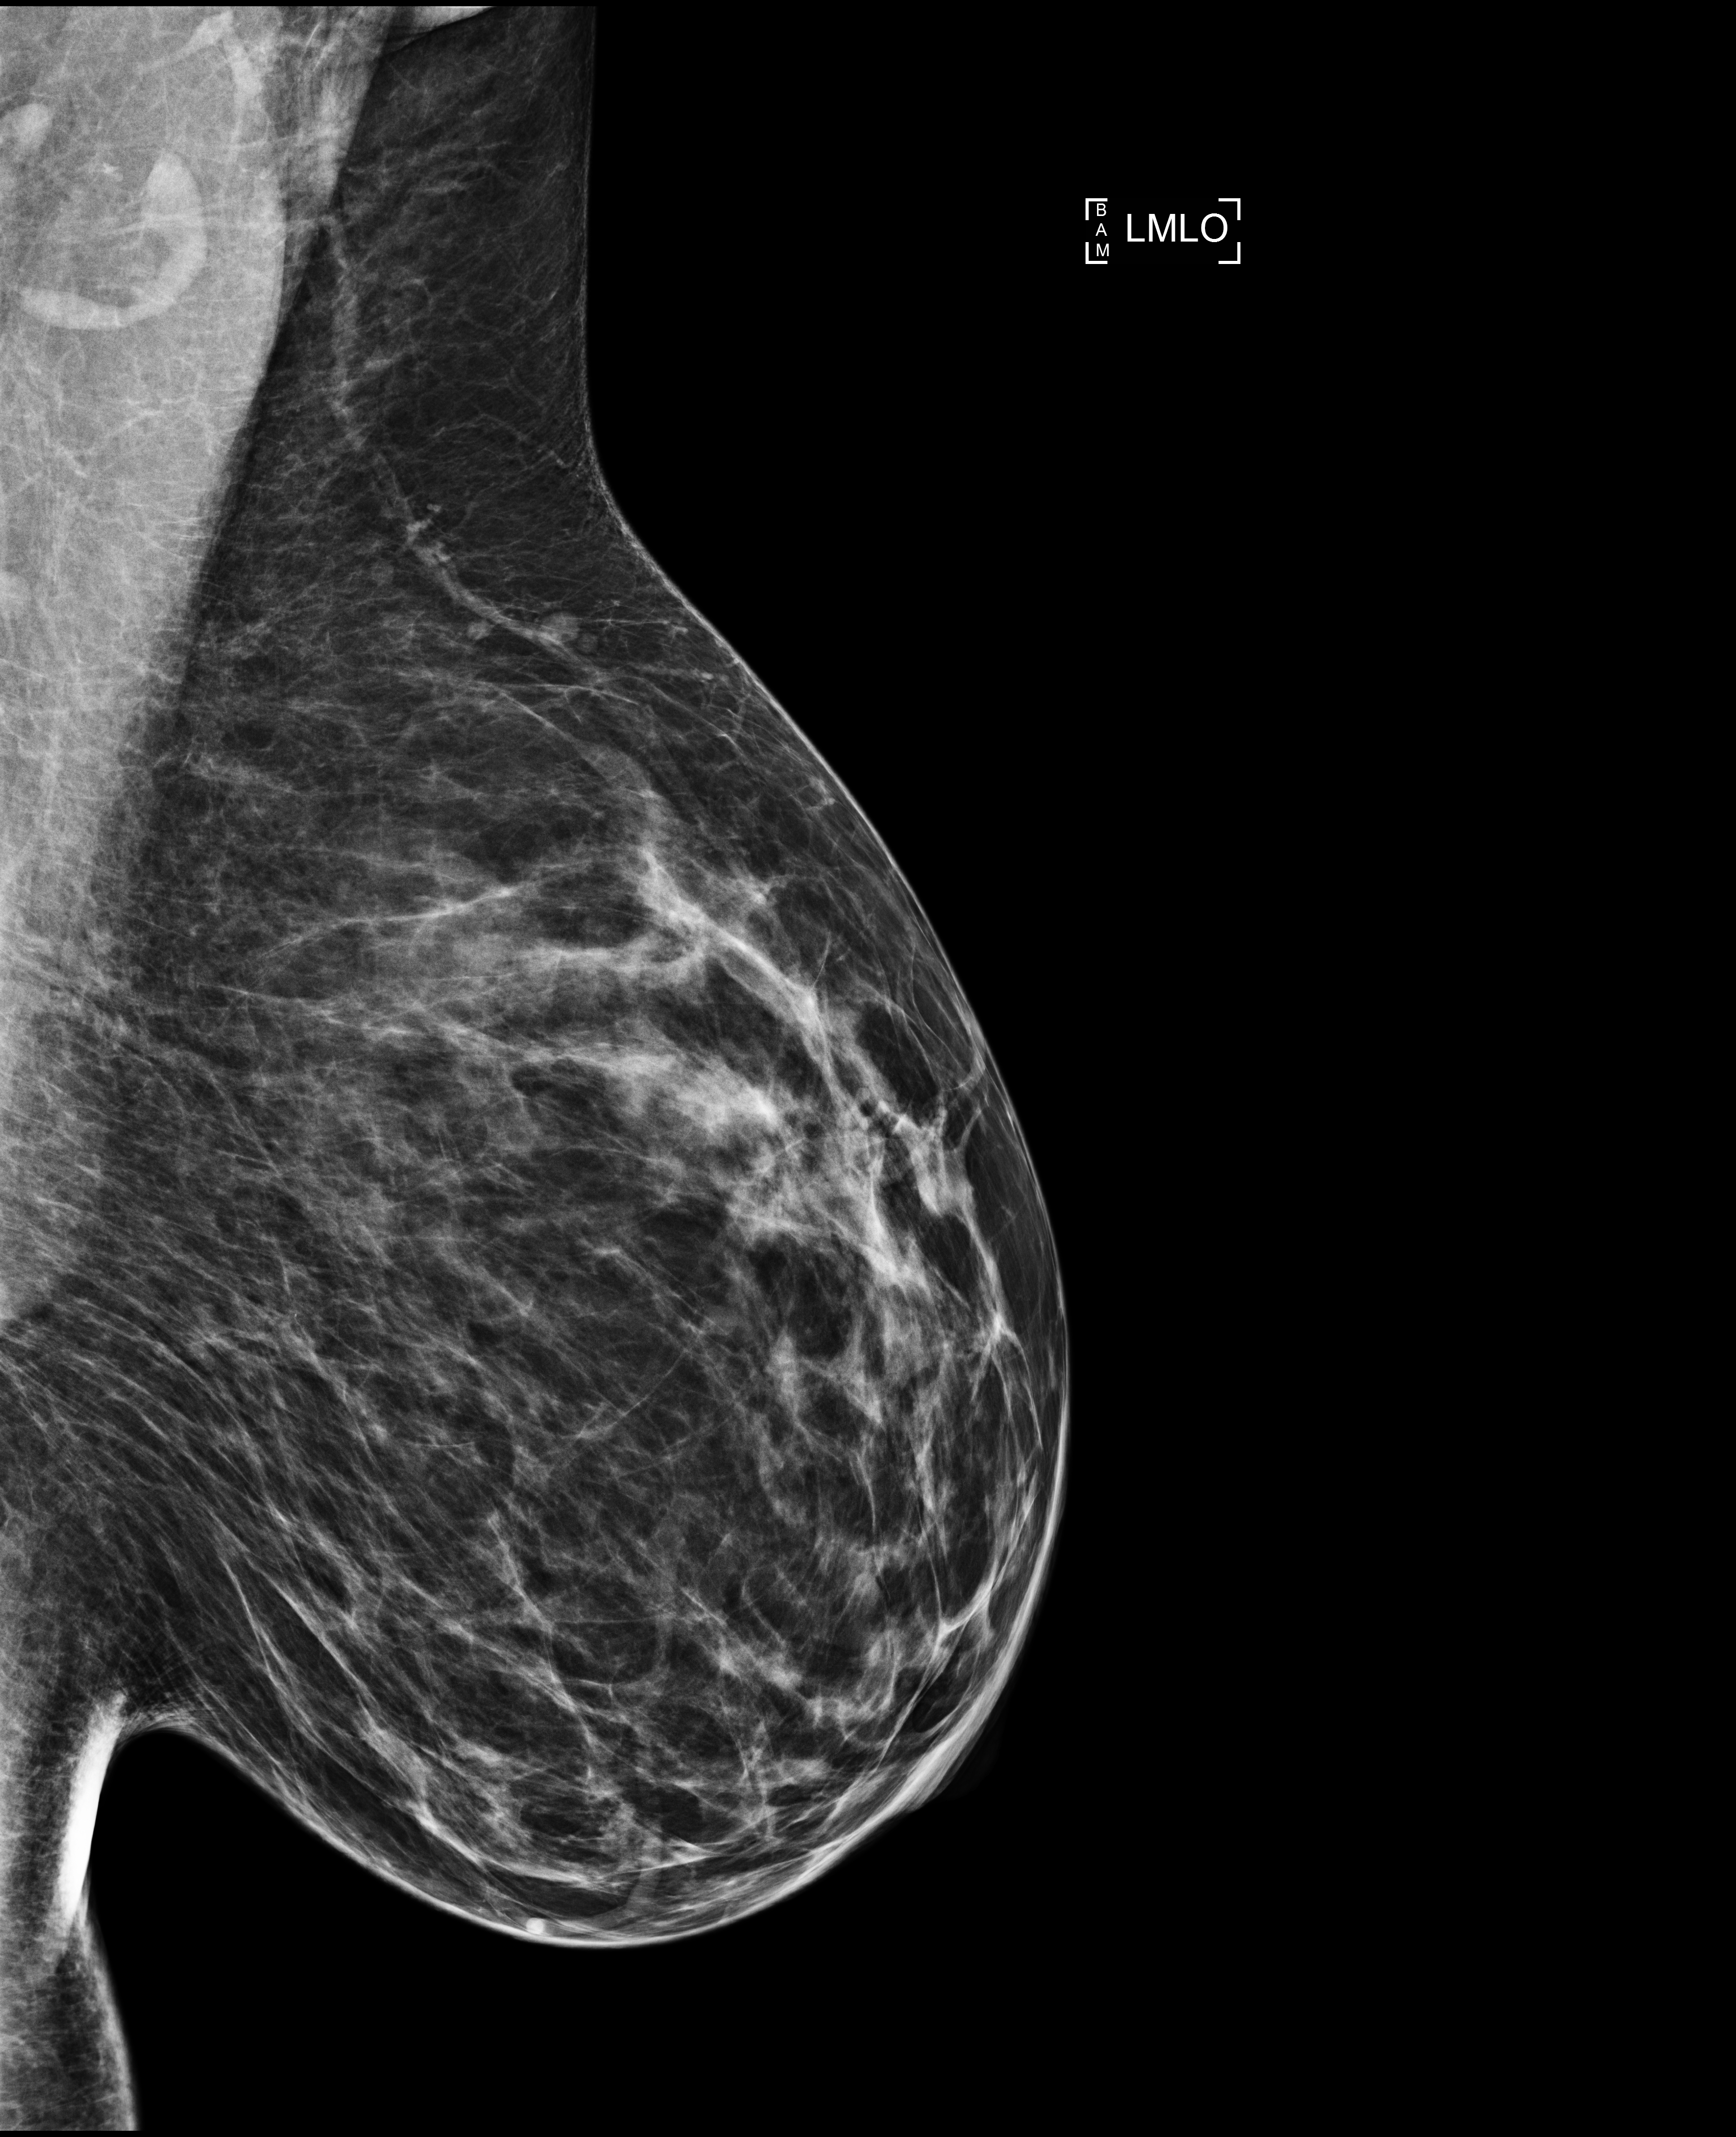
Full-field digital mammogram (FFDM); left breast; medio-lateral oblique projection; annual screening mammography examination; compressed breast thickness 74 mm; system: Selenia Dimensions. Female patient, age 42 years.
Final BI-RADS category for the screening round (tomosynthesis exam, both breasts): category 1.